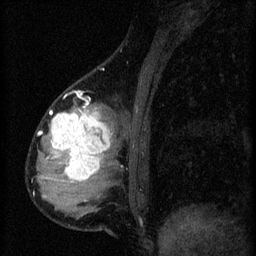
Breast MRI (dynamic contrast-enhanced), one sagittal slice; position 18 of 60 along the scan axis; 3 images stored at this slice position (order not interpretable as contrast timing); 1.5 T; TE 4.2 ms, TR 8.2 ms; 2 mm slice thickness; 256 × 256 image matrix, field of view 180 × 180 mm. Patient: female, 37 years.
Annotated regions visible in this slice (semi-automatically segmented with operator editing):
- analysis volume of interest (the breast-tissue region the enhancement analysis was run in; not a lesion): box from (x=44, y=100) to (x=119, y=197) px
- tumour enhancement mask (voxels above the 70 % enhancement threshold inside the analysis volume of interest): (x=51, y=106)–(x=113, y=181)